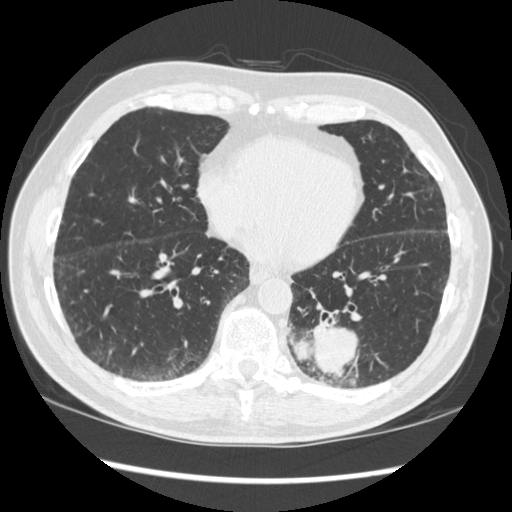
Low-dose screening chest CT, one axial slice. Position 120 of 348 along the scan axis. 120 kVp. Lung window (W 1500 / L -600 HU). 512 × 512 image matrix, field of view 360 × 360 mm.
Outlined on this slice (manually delineated by an expert):
- lesion 1 (tumor, lower lobe of left lung): box from (x=291, y=318) to (x=358, y=378) px